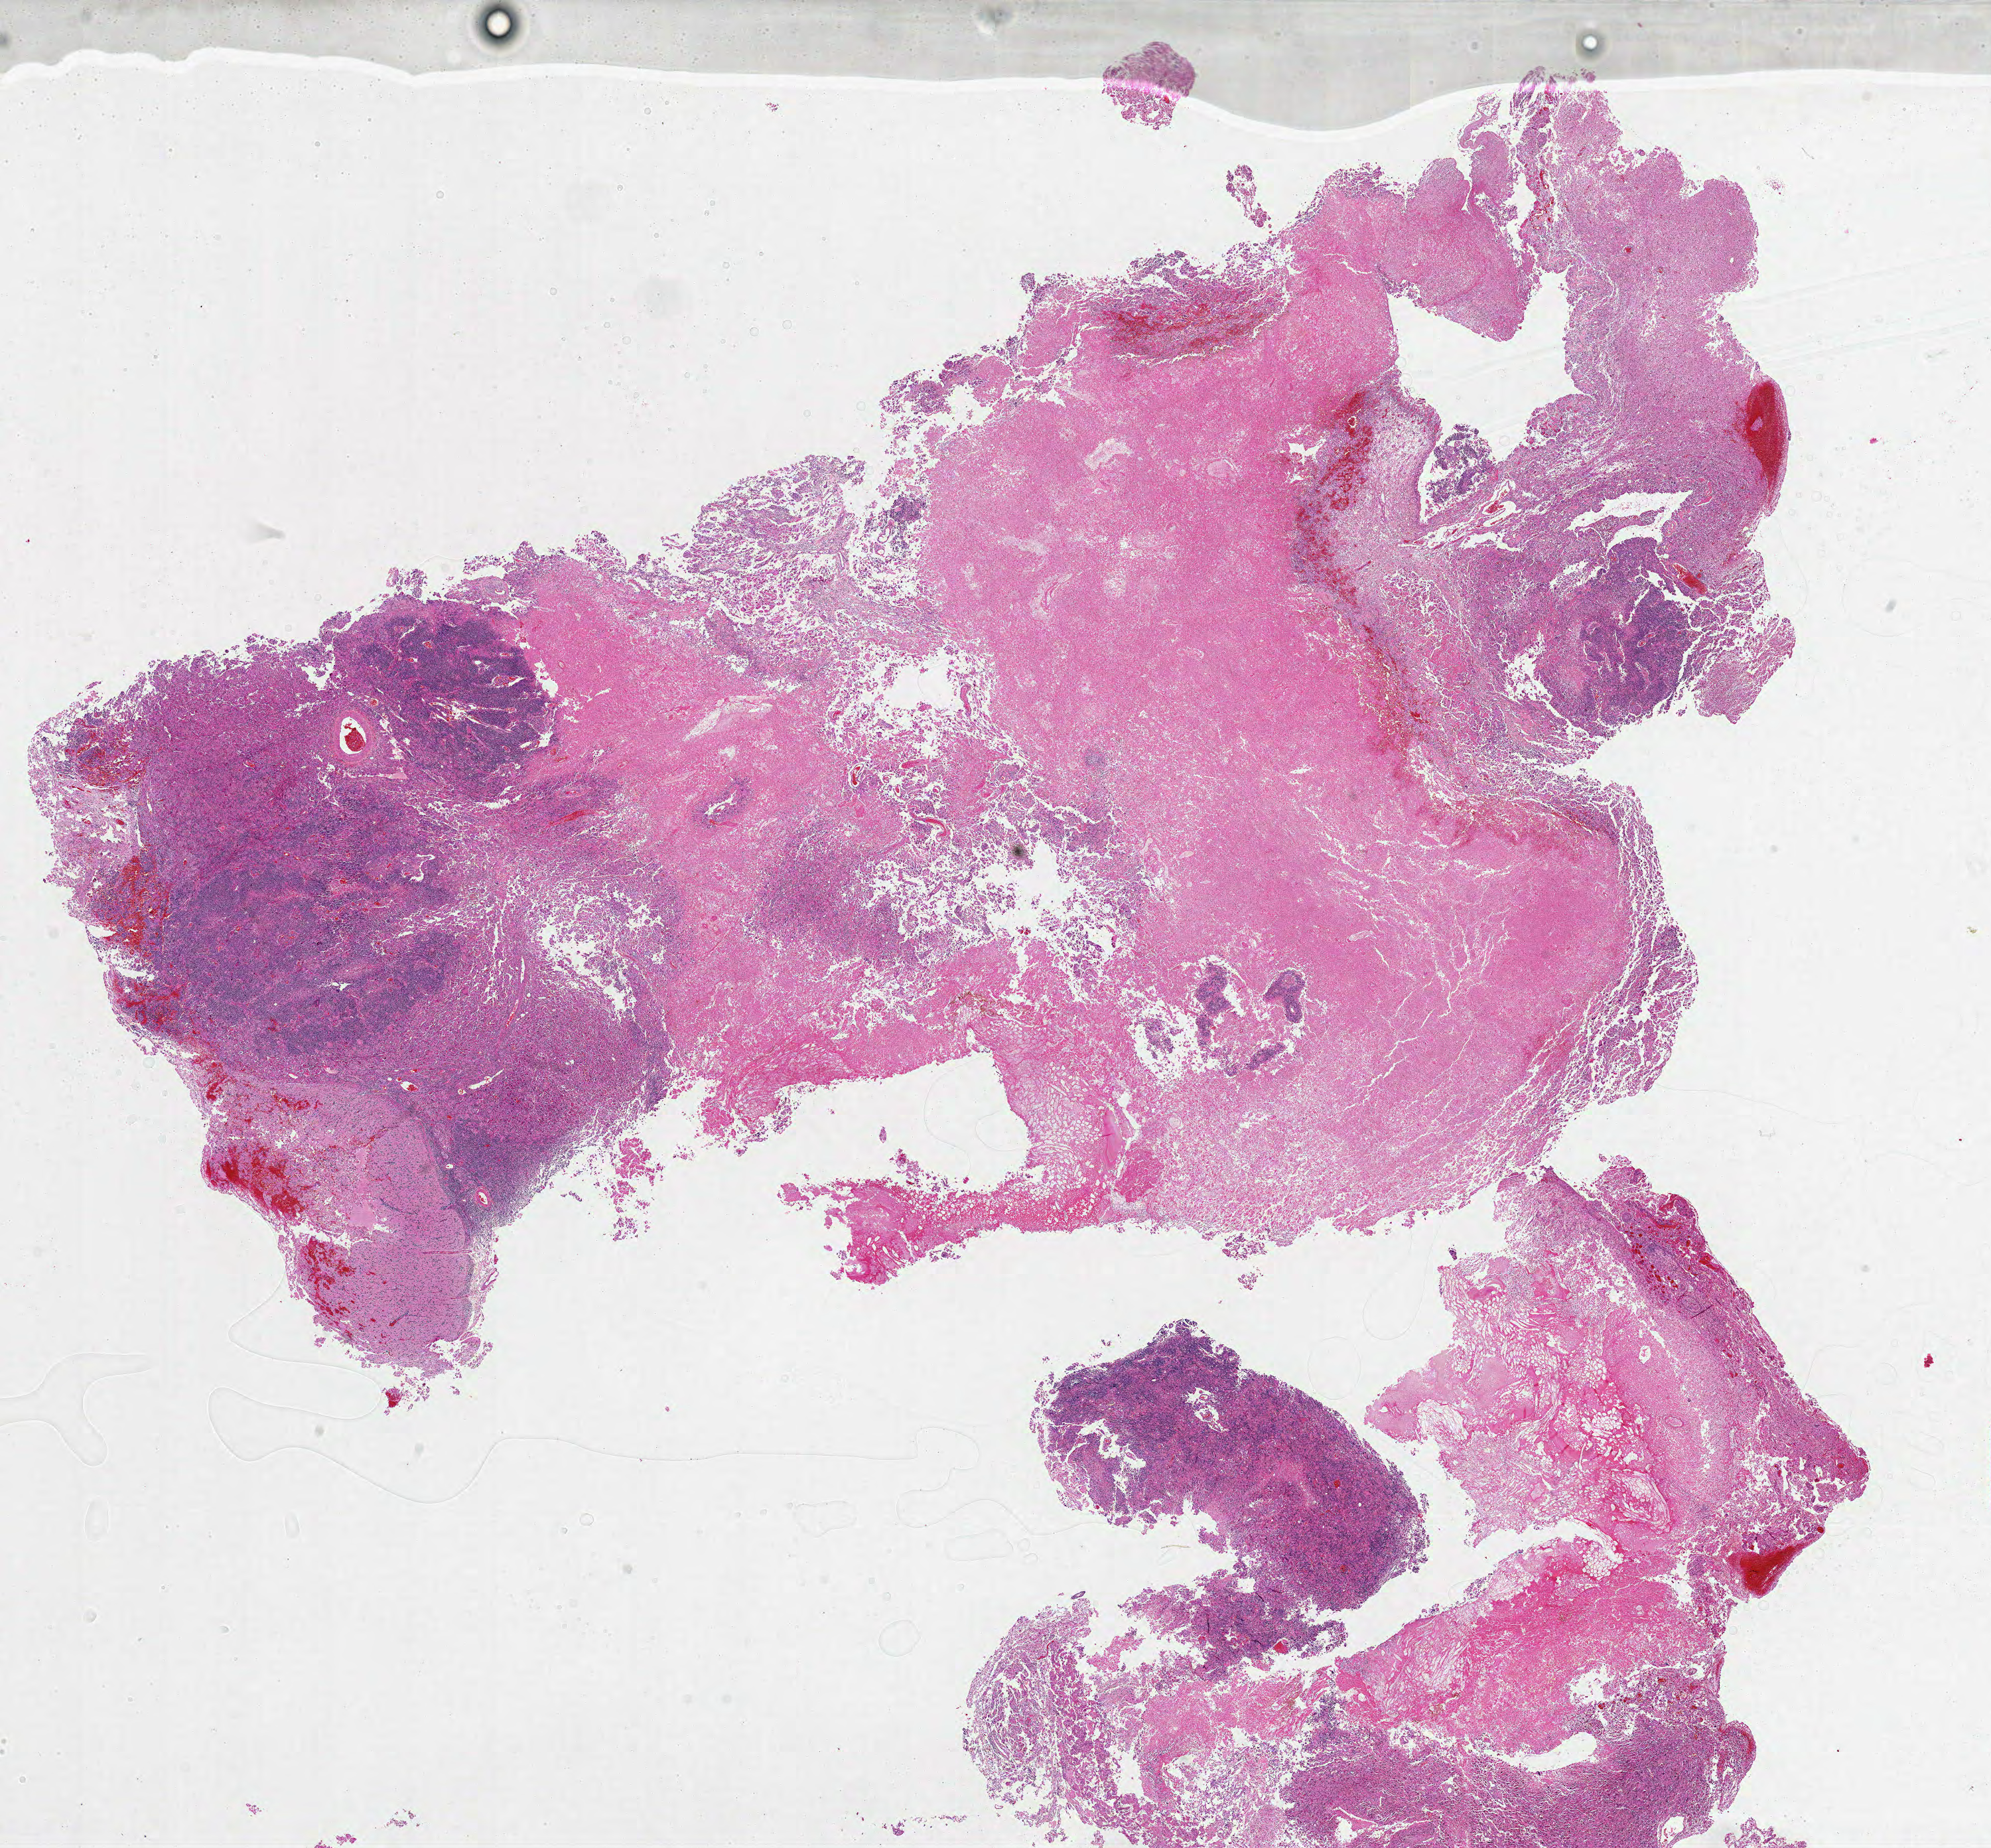
H&E-stained whole-slide image — shown as a low-resolution overview of the whole scanned area (about 24.0 x 22.2 mm). FFPE section. Brain, primary tumour sample. Male, age 24 years at initial diagnosis.
* pathologic diagnosis: Glioblastoma